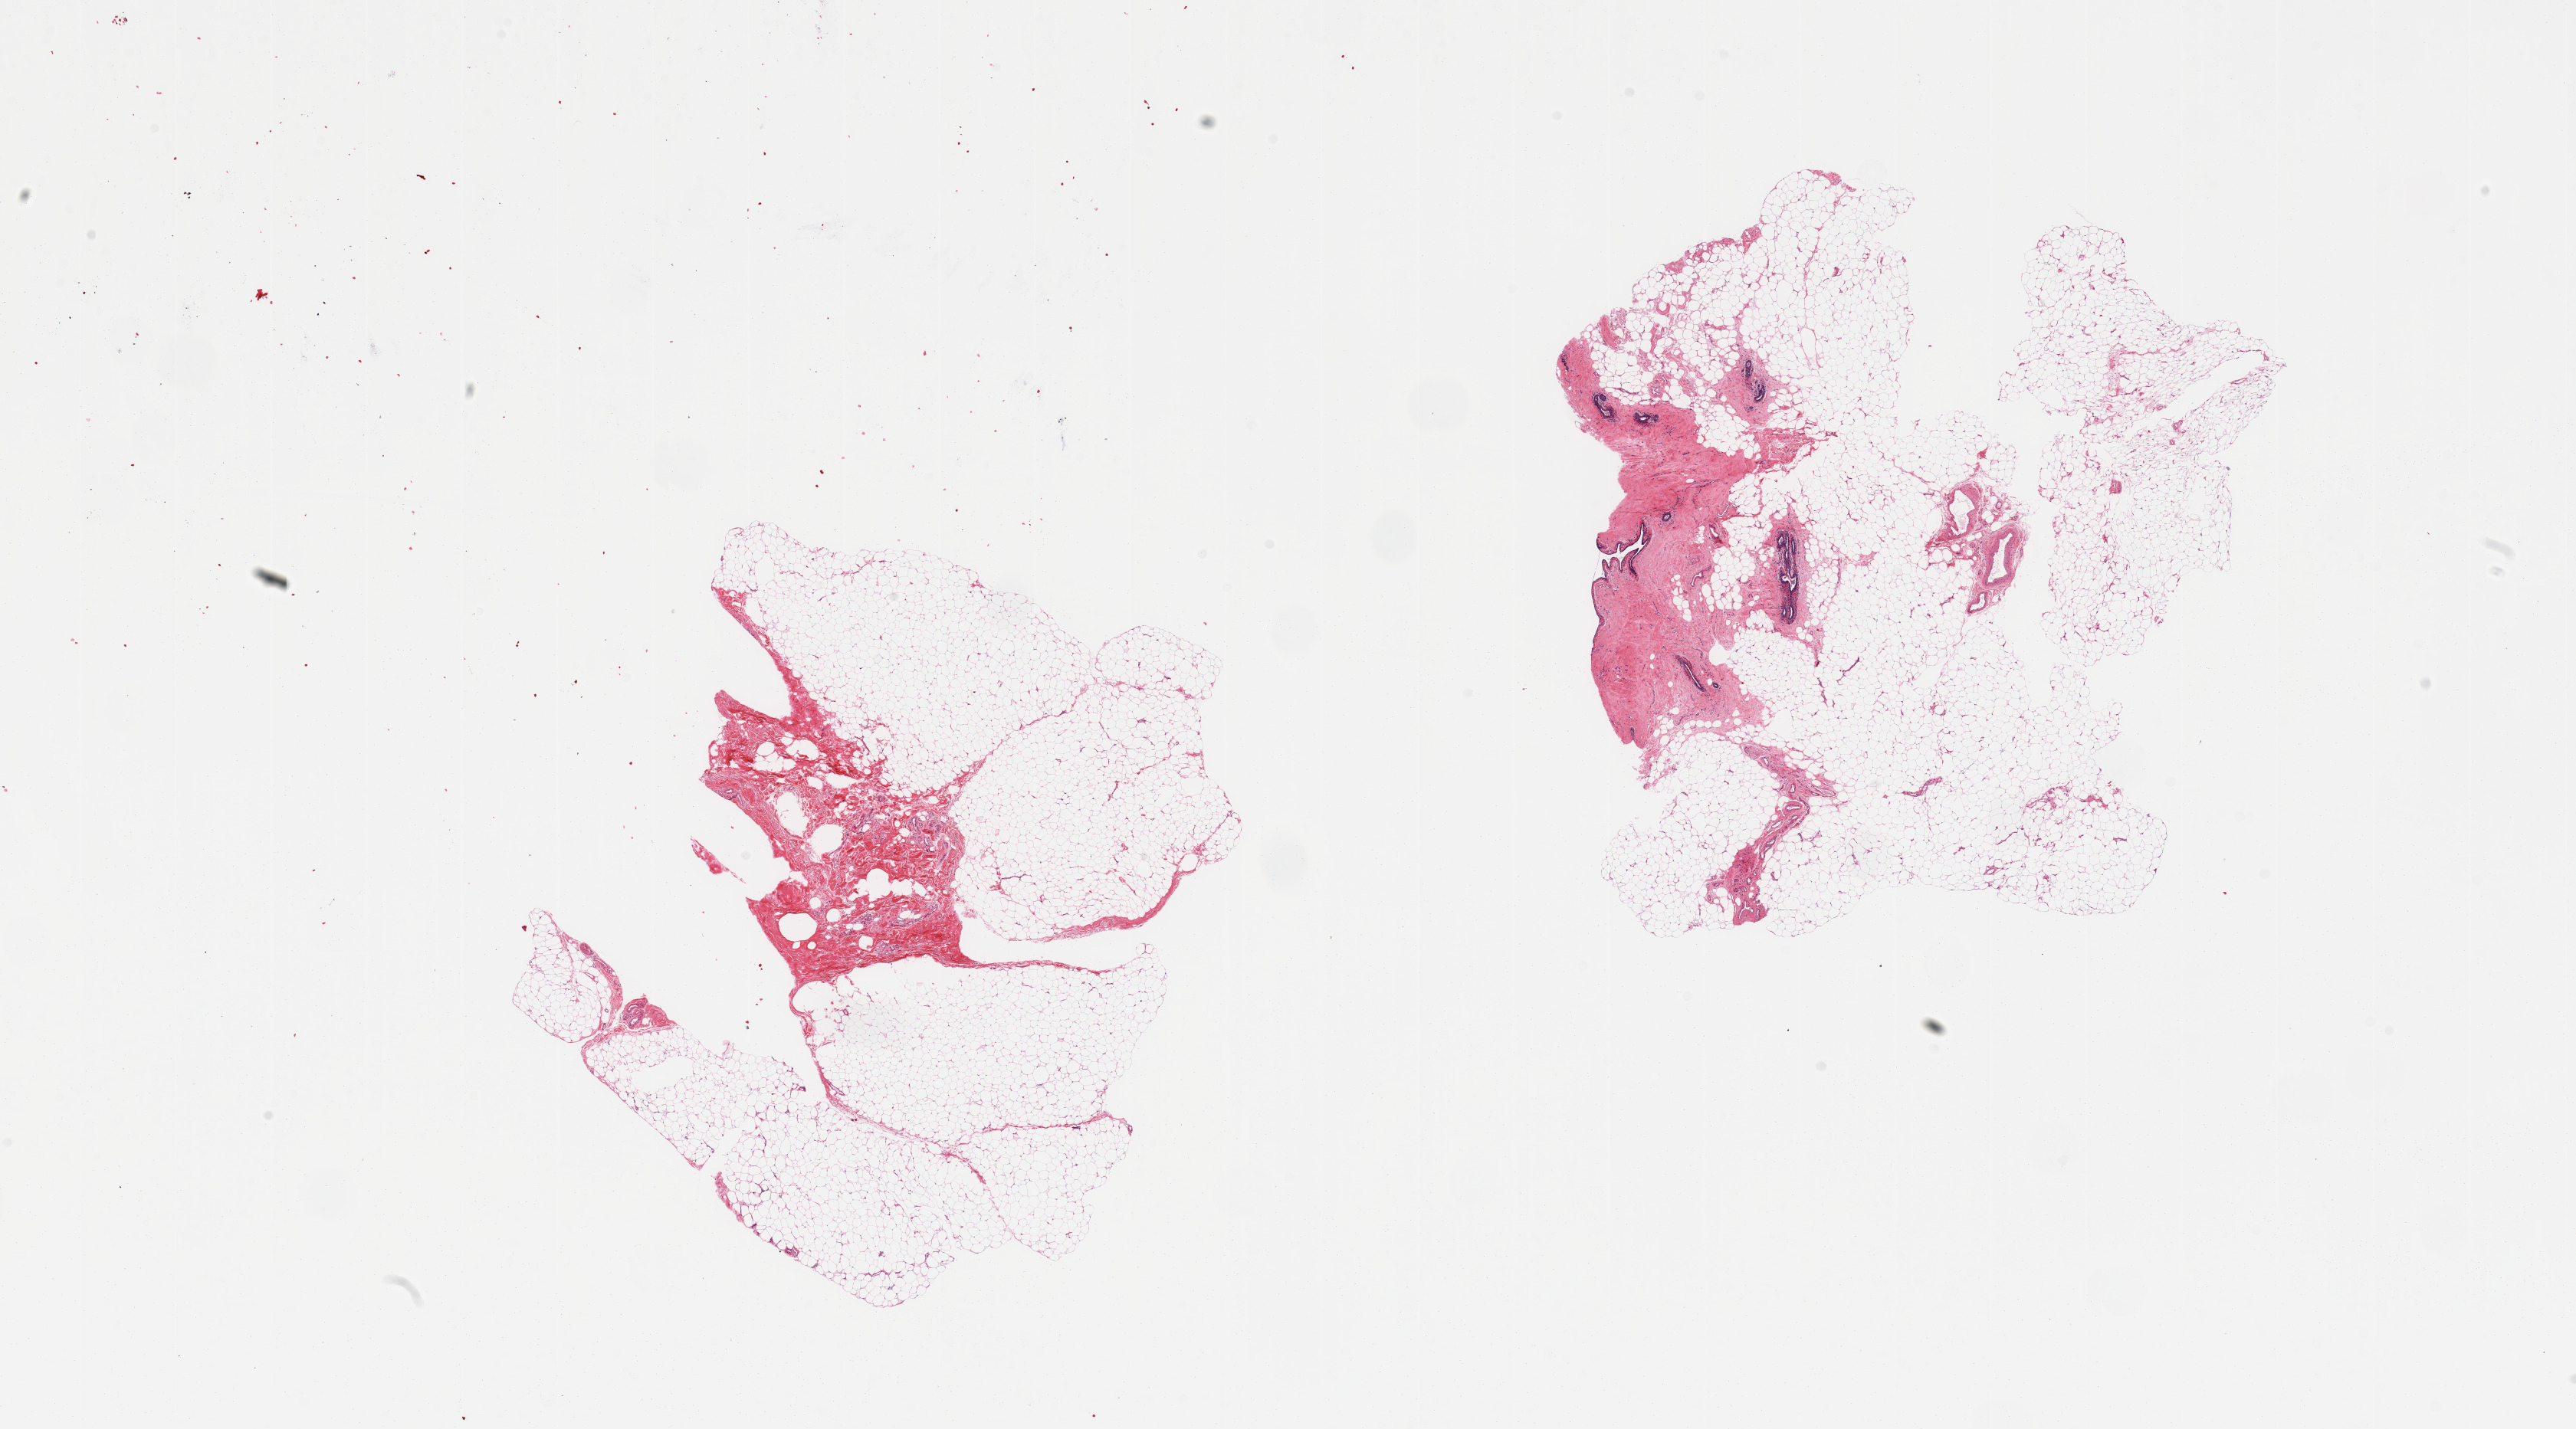
Whole-slide image, hematoxylin and eosin (H&E) stain, a low-resolution overview of the entire scanned area, about 26.6 x 14.7 mm (from a 20x scan), PAXgene-fixed paraffin-embedded (PFPE) section, section of breast (target tissue), tissue donor sample.
Review note (as recorded): 2 pieces; atrophic fatty mammary tissue.